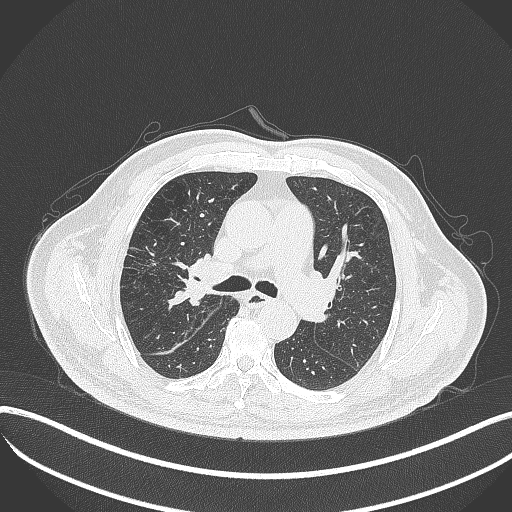
Chest CT, one axial slice. Position 228 of 401 along the scan axis. Reconstruction kernel B70f. Lung window (W 1500 / L -600 HU). 1 mm slice thickness. 512 × 512 image matrix. Patient: male, 72 years. From the clinical record (not read from this slice): clinical TNM (as recorded): T1c N0 M0; histopathological grade: G2.
Outlined on this slice (bounding box drawn by a radiologist):
- lung tumour (recorded histology: squamous cell carcinoma): bounding box [x1, y1, x2, y2] px = [169, 255, 209, 308]